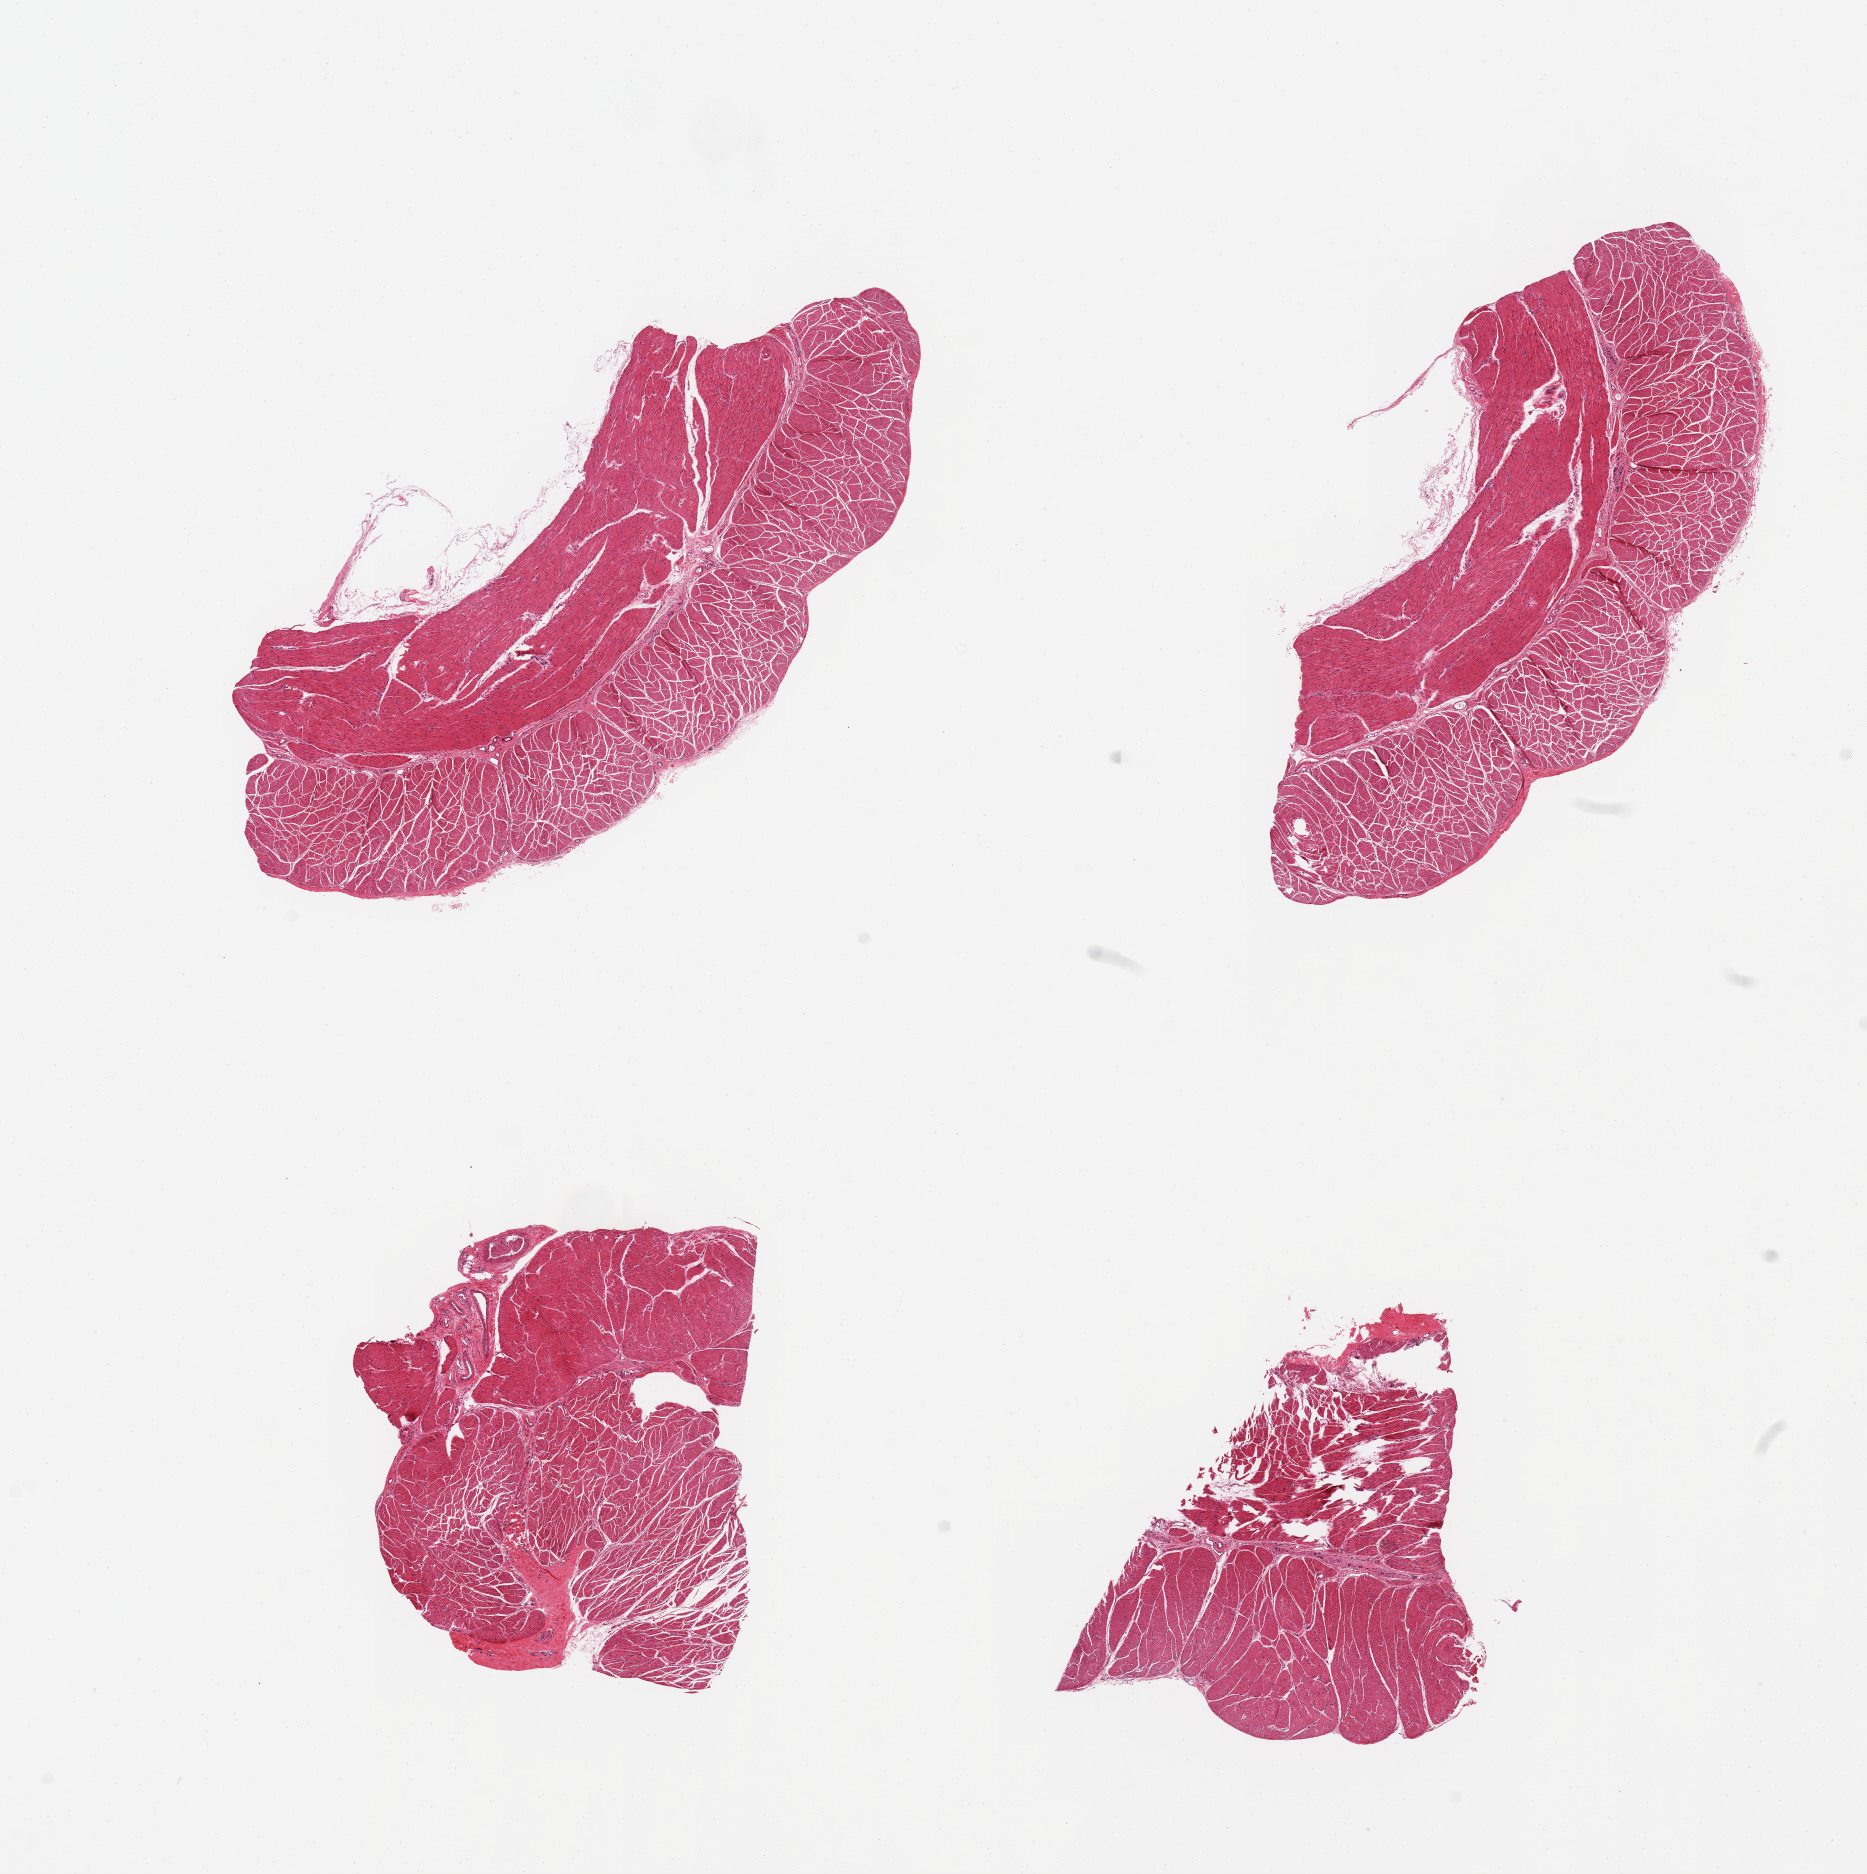
Digitized haematoxylin and eosin-stained section — low-resolution overview of the scanned area, about 14.8 x 14.8 mm. PAXgene-fixed, paraffin-embedded tissue. Sampled site (target tissue): esophageal muscle. Tissue donor sample. Donor sex: male.
Review note (as recorded): 4 pieces, target mucsuclaris obtained.